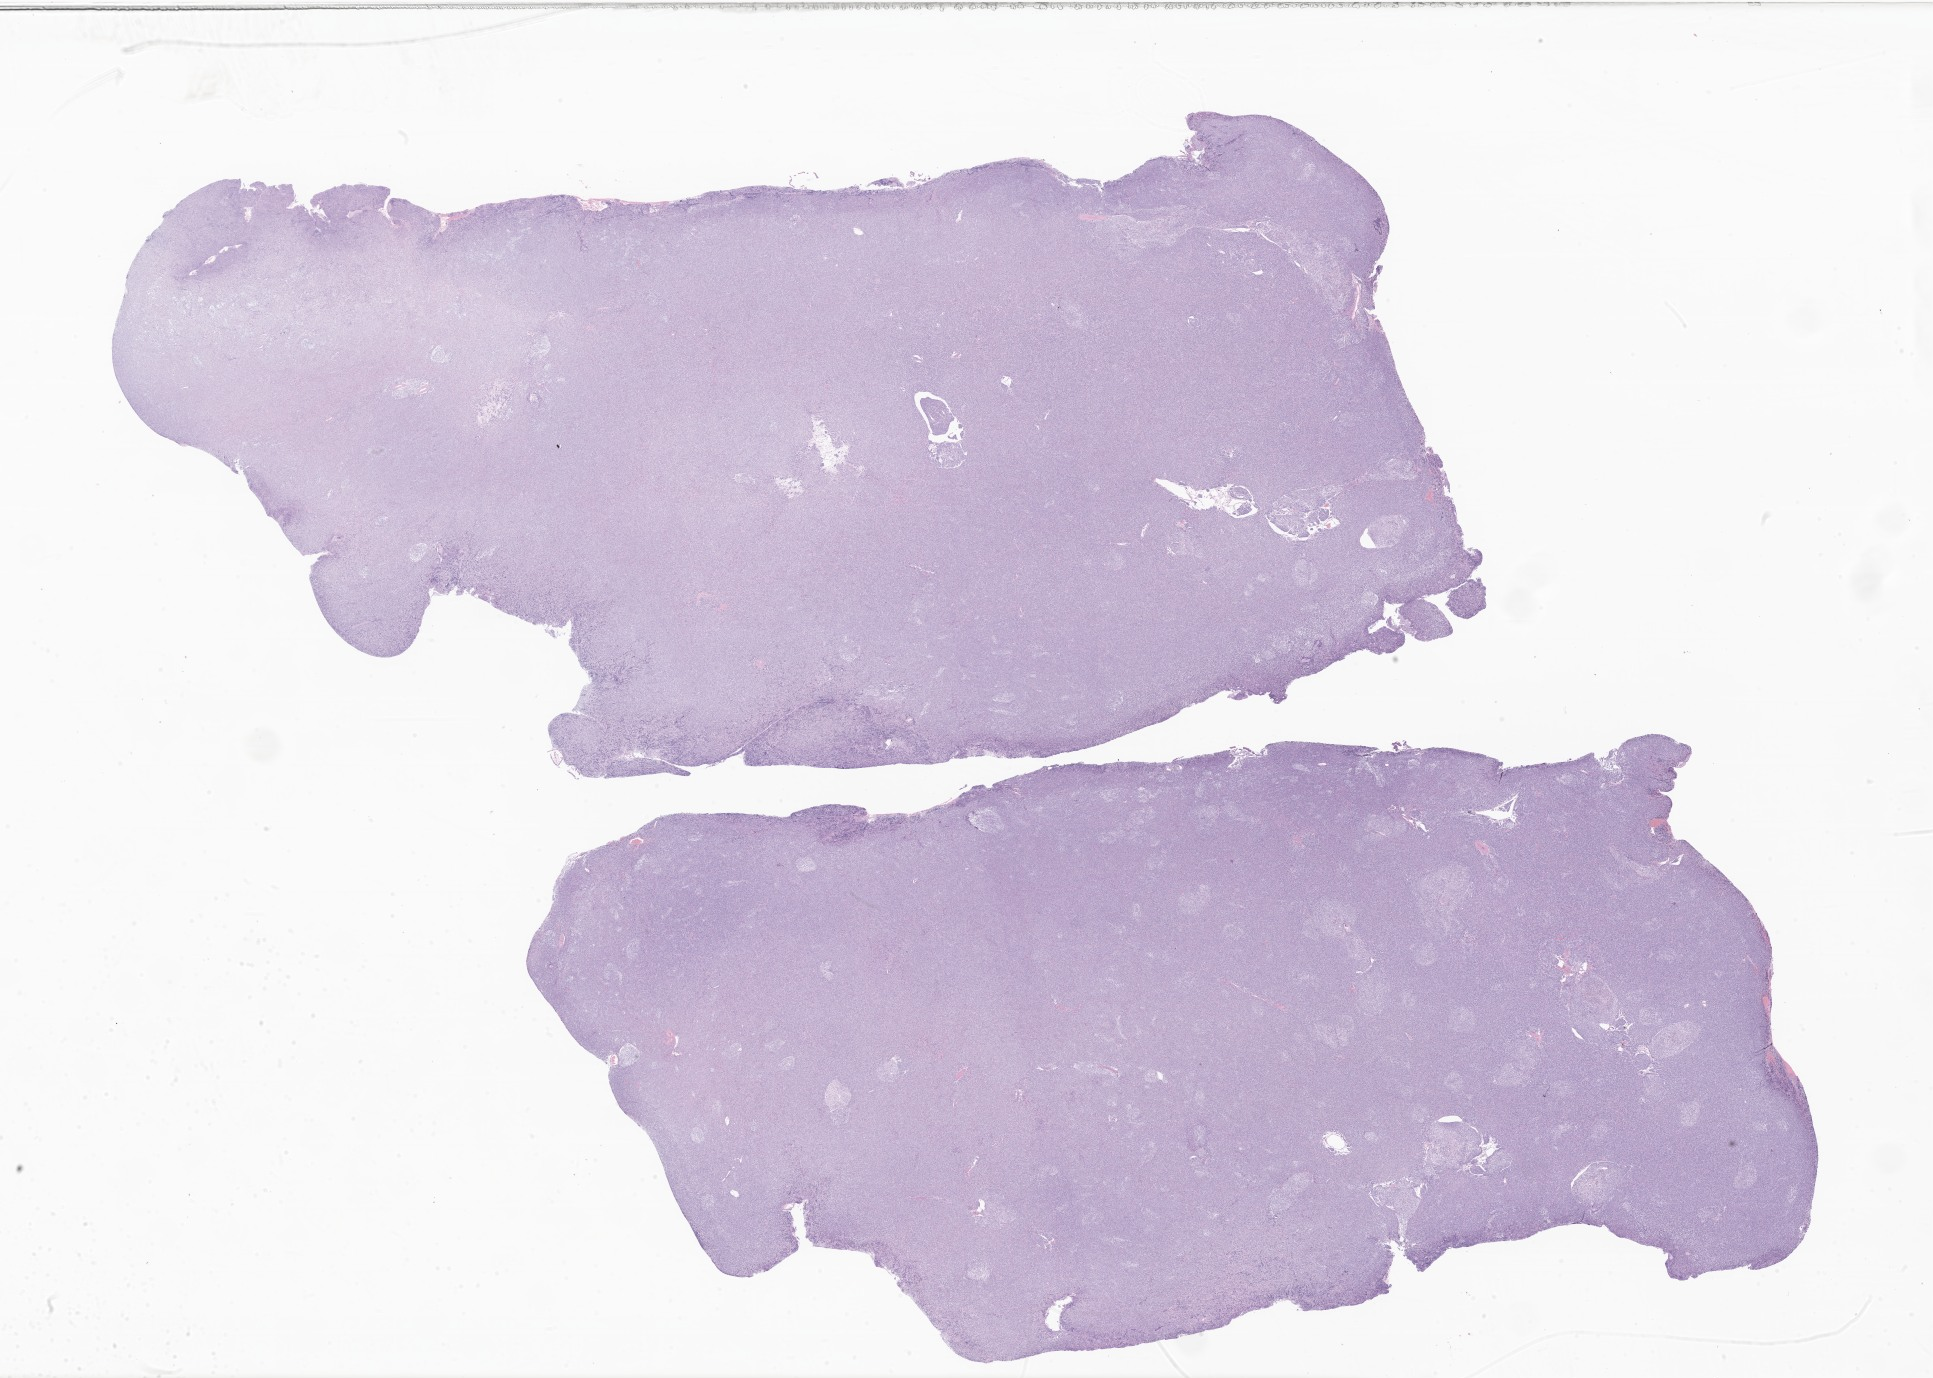
Digitized haematoxylin and eosin-stained section of tumor tissue from the brain — whole scanned area (about 32.6 x 23.2 mm) shown as a low-resolution overview. Formalin-fixed paraffin-embedded section. Female patient, age 46 months (3 years 10 months).
Recorded diagnosis: Desmoplastic nodular medulloblastoma.